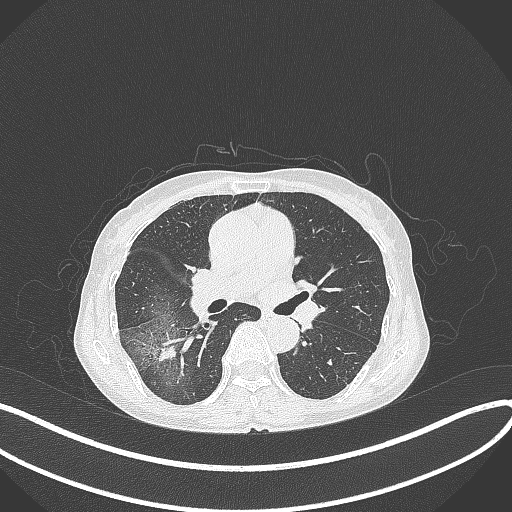
Chest CT, one axial slice. Slice 222 of 371 in the series (ordered by position). Reconstruction kernel B70f. 120 kVp. Lung window (W 1500 / L -600 HU). 512 × 512 image matrix, field of view 400 × 400 mm. Patient: female, 69 years. Case-level facts recorded for this patient, not image findings: clinical TNM (as recorded): T1b N0 M0.
Annotated regions visible in this slice (rectangle marked by the reading radiologist):
- lung tumour (recorded histology: adenocarcinoma): bounding box [x1, y1, x2, y2] px = [153, 340, 181, 363]